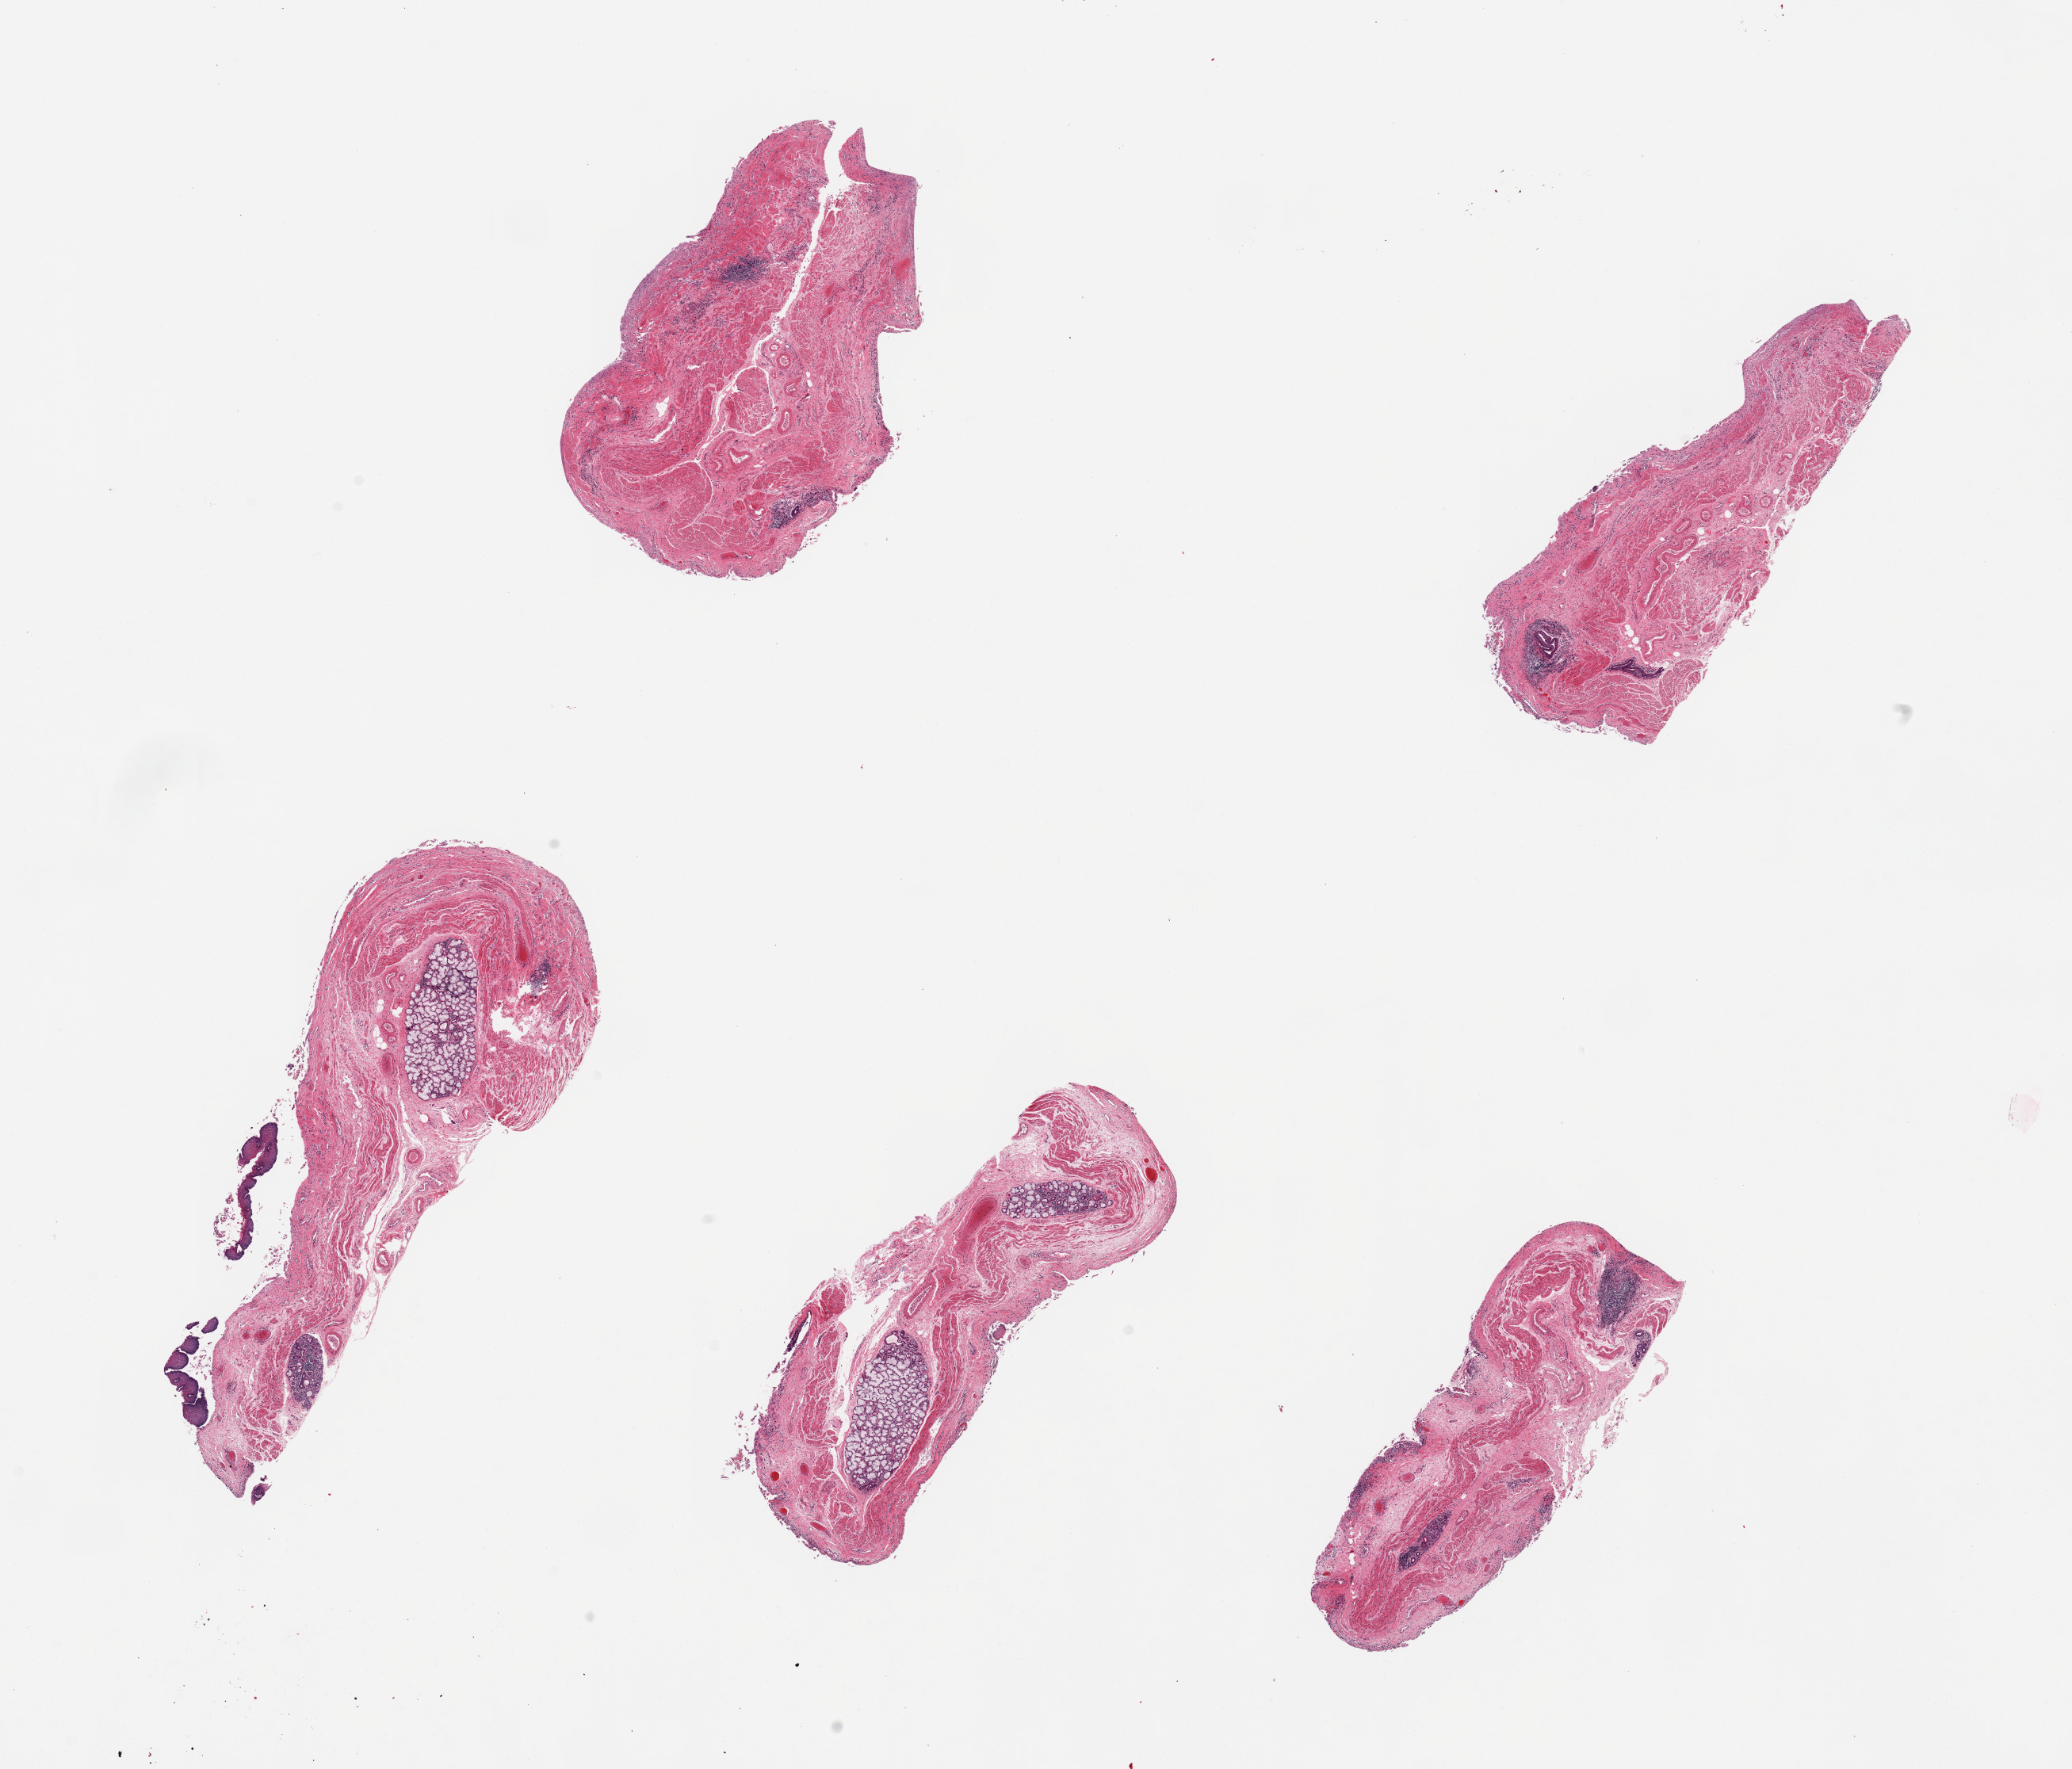
Digitized H&E-stained section, brightfield, a low-resolution overview of the entire scanned area, about 20.7 x 17.7 mm (from a 20x scan), PAXgene-fixed paraffin-embedded (PFPE) section, target tissue: esophageal mucous membrane, donor tissue sample.
Reviewer comment on this tissue sample: 5 pieces; only one piece includes squamous epithelium which is fragmented and detached; patchy chronic inflammation and focal lymphocytic aggregate with foreign body giant cell.